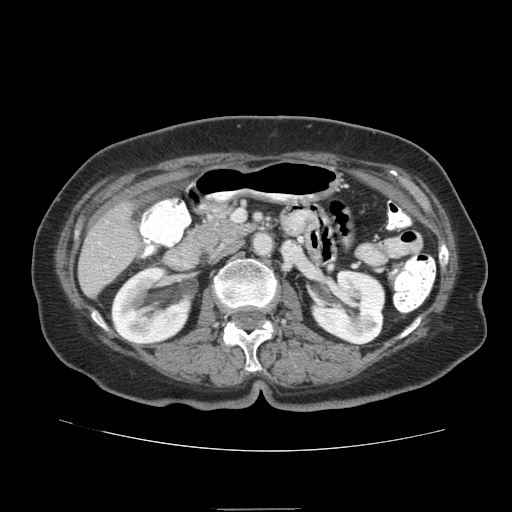
Contrast-enhanced abdominal CT (liver protocol), one axial slice. Position 30 of 95 along the scan axis. Reconstruction kernel STANDARD. 140 kVp. Soft-tissue window (W 400 / L 40 HU). 2.5 mm slice thickness. 512 × 512 image matrix, field of view 360 × 360 mm. Case-level facts recorded for this patient, not image findings: diagnosis: hepatocellular carcinoma (patient treated with transarterial chemoembolisation; whether this scan precedes or follows treatment is not stated here); TNM stage (as recorded): Stage-IVA; Child-Pugh class: B; tumour differentiation: moderately differentiated.
Structures marked on this image (semi-automatic segmentation, software-assisted and operator-edited):
- liver parenchyma outside the tumour (the mass and vessels are separate outlines, so this box may not span the whole liver): bounding box (x1, y1, x2, y2) in pixels: (78, 202, 140, 296)